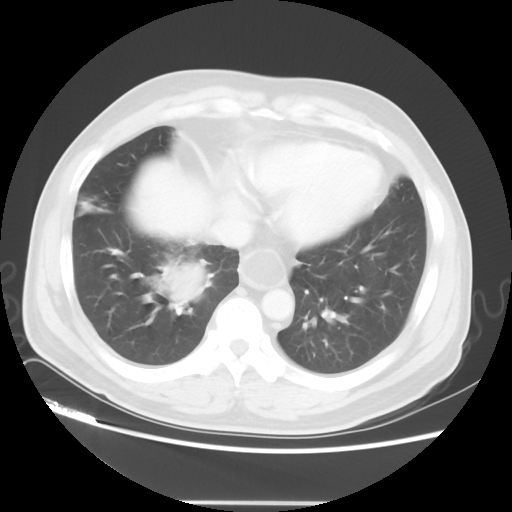
Chest CT, one axial slice; slice 15 of 48 in the series (ordered by position); 120 kVp; lung window (W 1500 / L -600 HU); 5 mm slice thickness; 512 × 512 image matrix. Male patient, age 53 years. Case-level facts recorded for this patient, not image findings: clinical TNM (as recorded): T2 N3 M0.
Outlined on this slice (bounding box drawn by a radiologist):
- lung tumour (recorded histology: small cell carcinoma): bounding box [x1, y1, x2, y2] px = [152, 256, 211, 315]